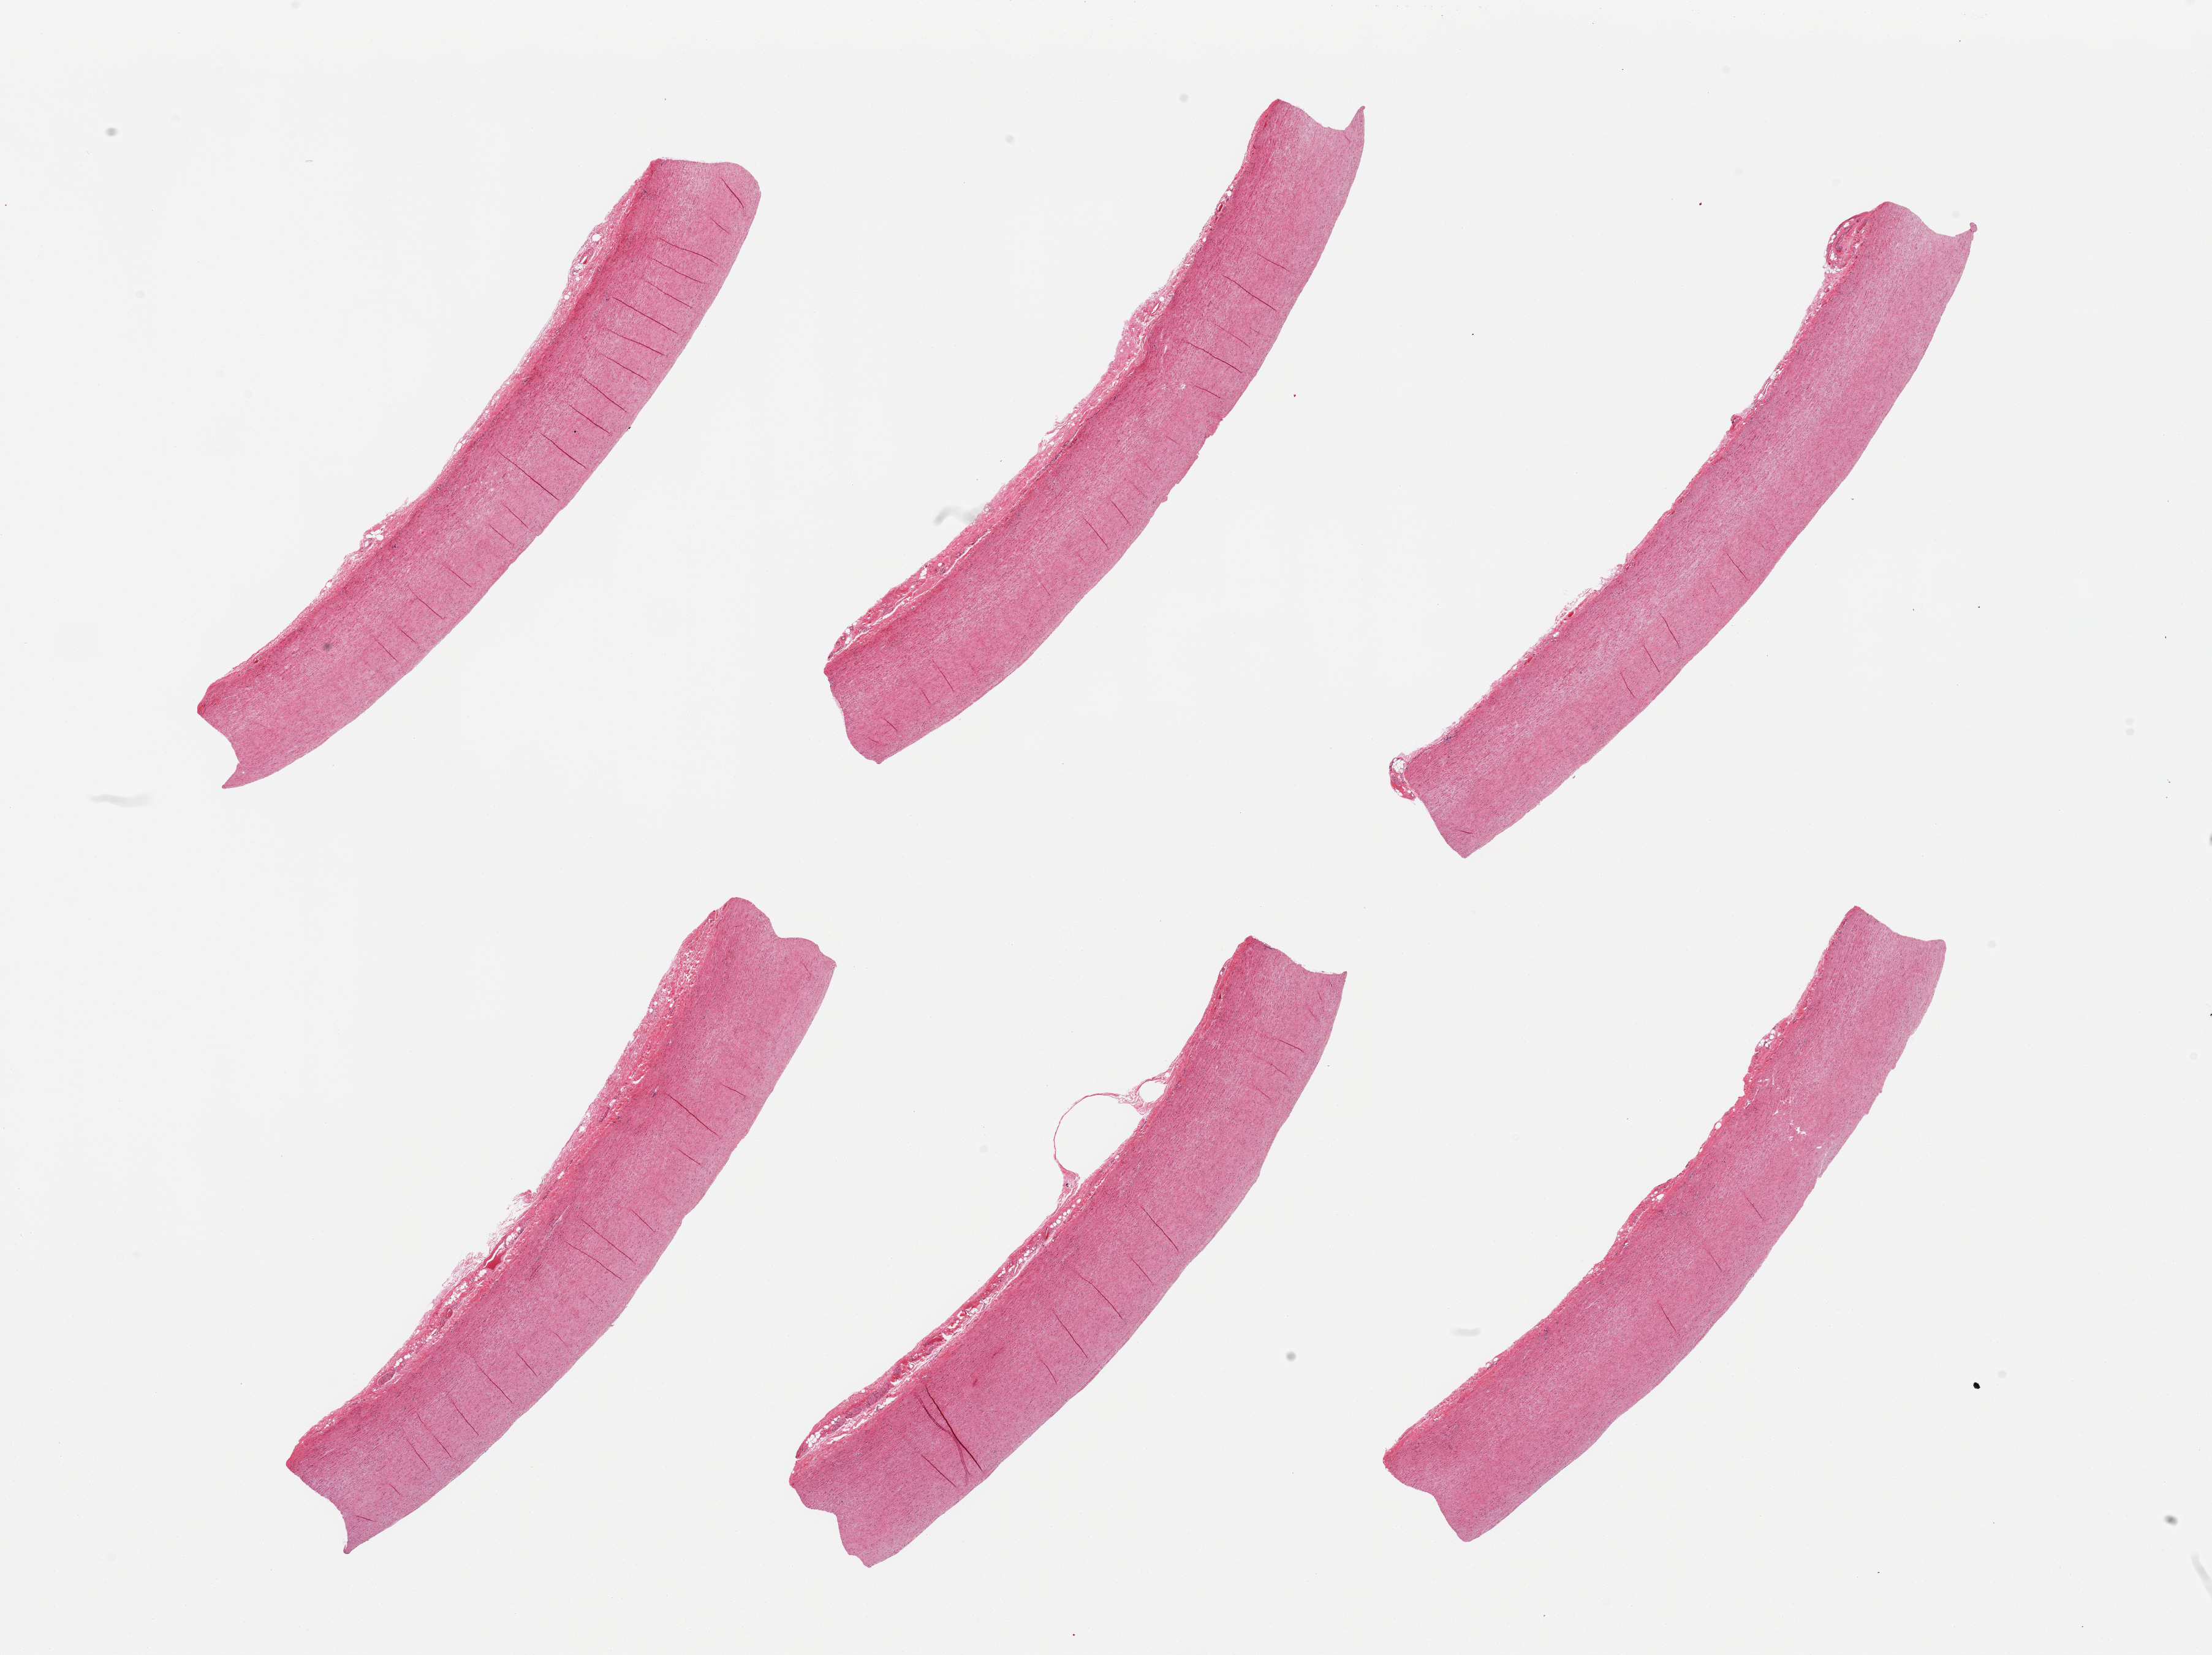
Digitized H&E-stained section — low-resolution overview of the scanned area, about 28.5 x 21.4 mm. PAXgene-fixed, paraffin-embedded tissue. Sampled site (target tissue): aorta. Donor tissue sample. Donor: male.
Pathologist's review note for this sample: 6 pieces.